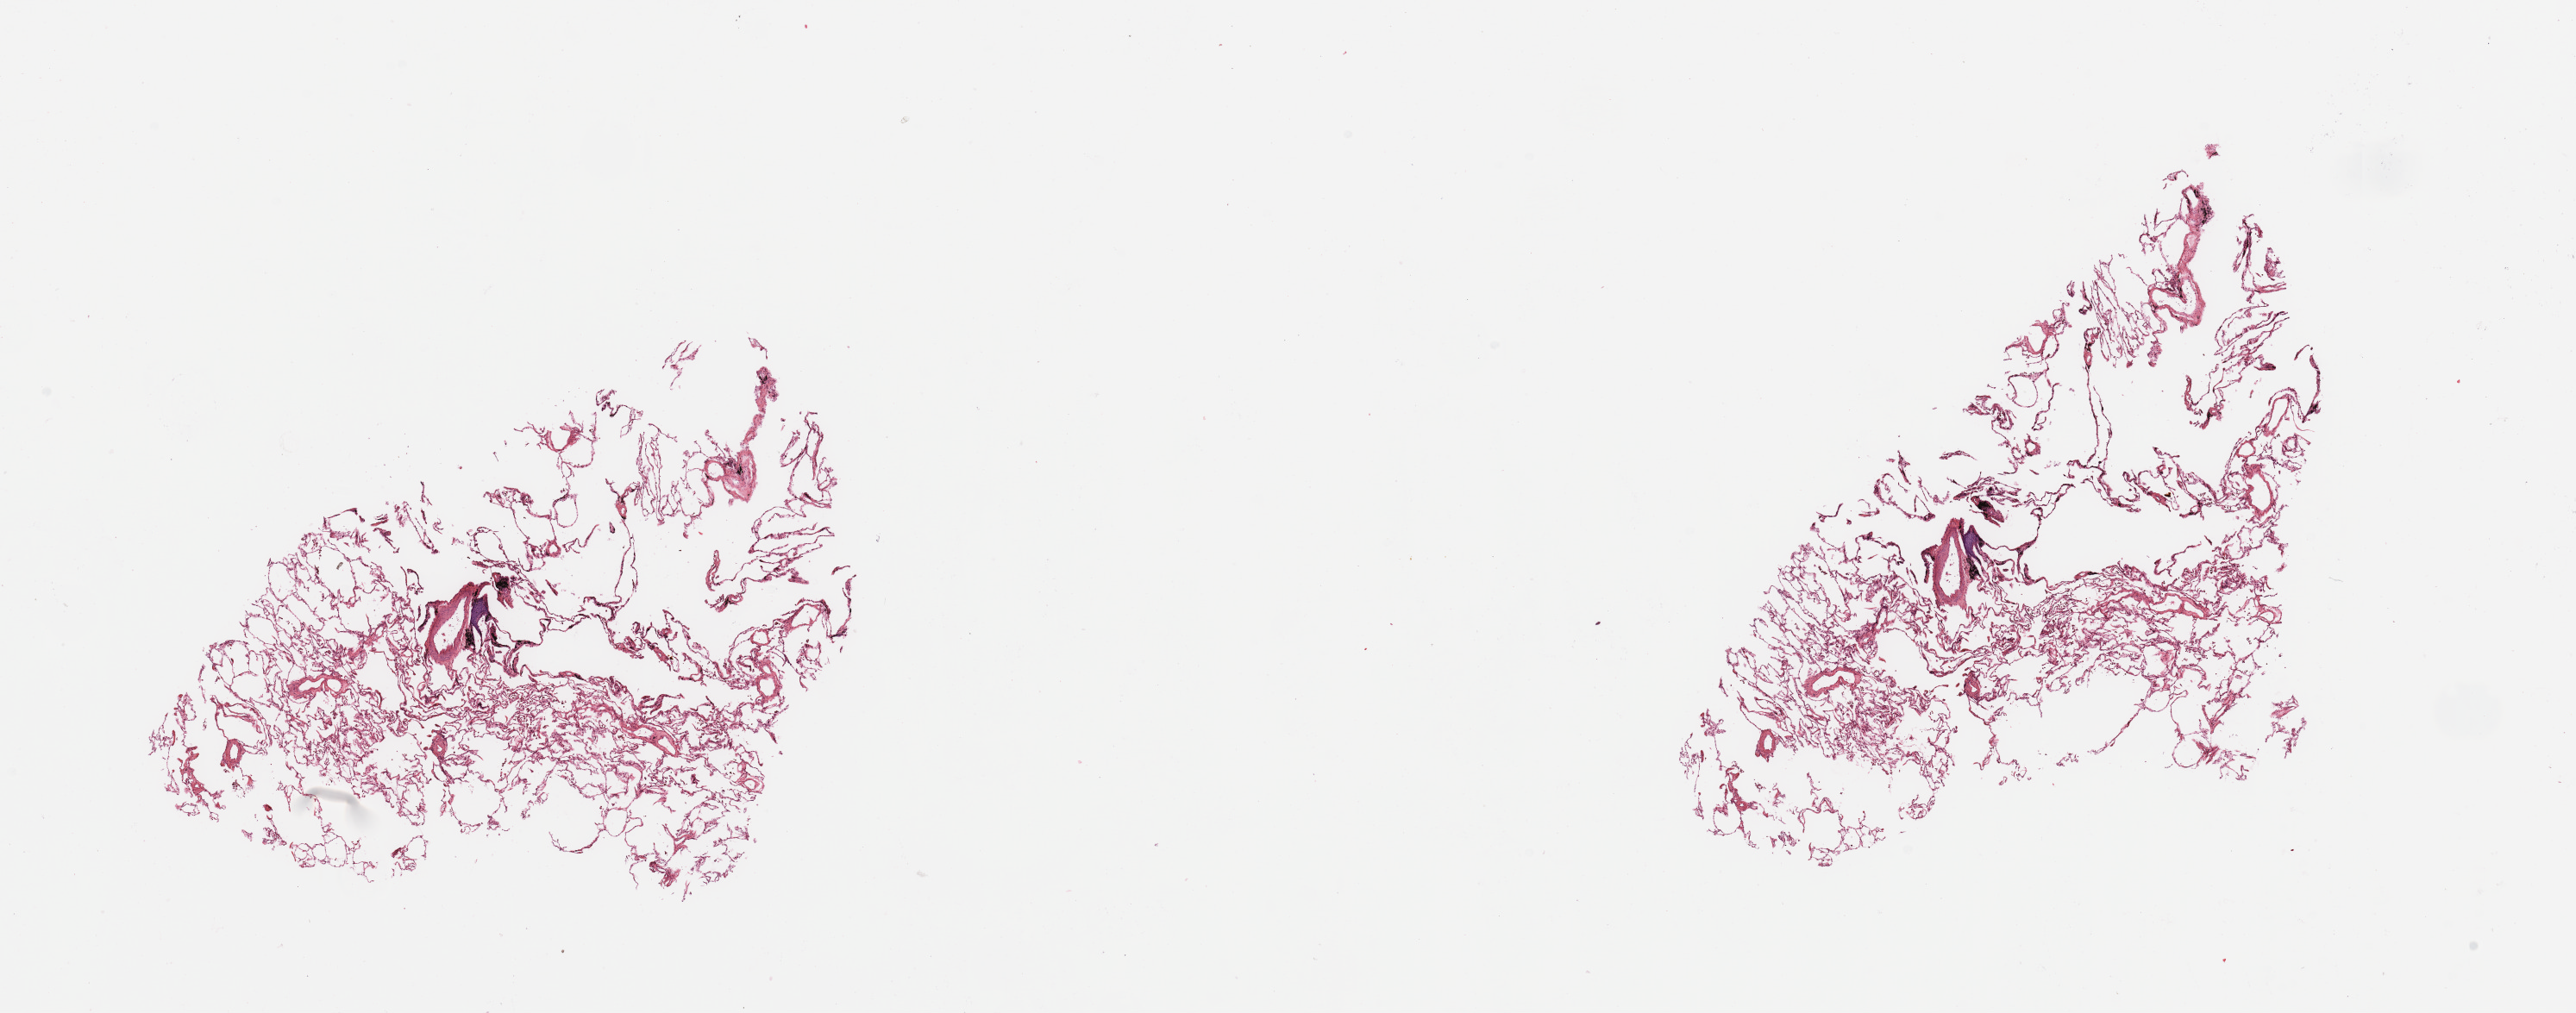
H&E-stained whole-slide image, whole scanned area (about 23.6 x 9.3 mm, from a 20x scan) shown as a low-resolution overview. Normal (non-tumour) tissue sample, sampled site: lung. Patient: male, age 67 years.
This section: normal (non-tumour) tissue from the same patient. Patient diagnosis: Squamous cell carcinoma, NOS.